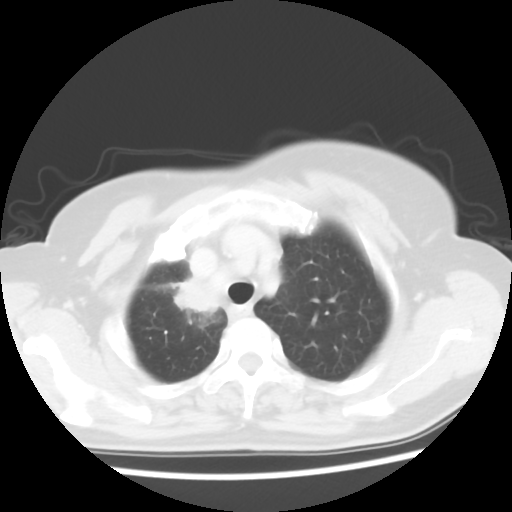
Chest CT, one axial slice. Slice 47 of 56 in the series (ordered by position). Reconstruction kernel STANDARD. 120 kVp. Lung window (W 1500 / L -600 HU). 512 × 512 image matrix, field of view 314 × 314 mm. Female patient, age 62 years. From the clinical record (not read from this slice): clinical TNM (as recorded): T2 N1 M1a.
Annotated regions visible in this slice (bounding box drawn by a radiologist):
- lung tumour (recorded histology: adenocarcinoma): bounding box <163,268,222,327> (left, top, right, bottom; pixels)